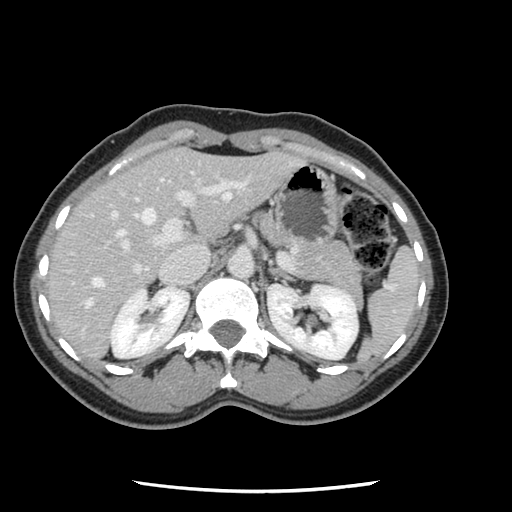
Contrast-enhanced abdominal CT, one axial slice. Position 75 of 134 along the scan axis. Intravenous contrast given. Soft-tissue window (W 400 / L 40 HU). 2.5 mm slice thickness. 512 × 512 image matrix, field of view 330 × 330 mm. Female patient, age 43 years. From the clinical record (not read from this slice): diagnosis: colorectal cancer liver metastases, imaged before liver resection.
Structures marked on this image (manually delineated by an expert):
- hepatic veins: bounding box (x1, y1, x2, y2) in pixels: (85, 179, 231, 308)
- liver: (47, 148, 297, 359)
- planned liver remnant (the part of the liver to remain after resection): (47, 151, 187, 304)
- portal vein (with intrahepatic branches): (72, 181, 246, 293)